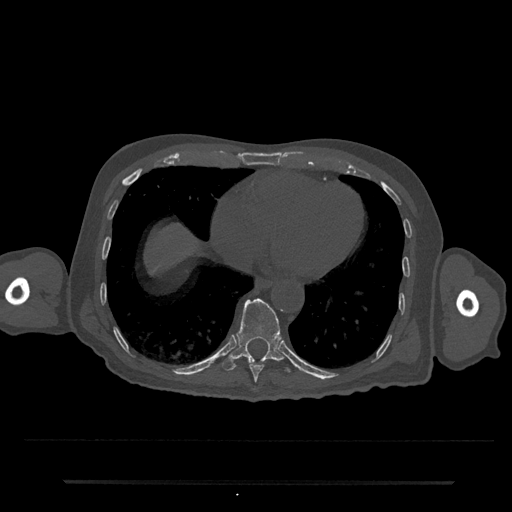
CT including the spine, one axial slice; slice 333 of 797 in the series (ordered by position); reconstruction kernel Br40s/3; 120 kVp; bone window (W 1800 / L 400 HU); 512 × 512 image matrix, field of view 427 × 427 mm. Male patient, age 74 years. Case-level facts recorded for this patient, not image findings: primary cancer: prostate.
Annotated regions visible in this slice (semi-automatic segmentation, software-assisted and operator-edited):
- T10 vertebra: bounding box <222,298,291,373> (left, top, right, bottom; pixels)
- T9 vertebra: <249,361,264,382>